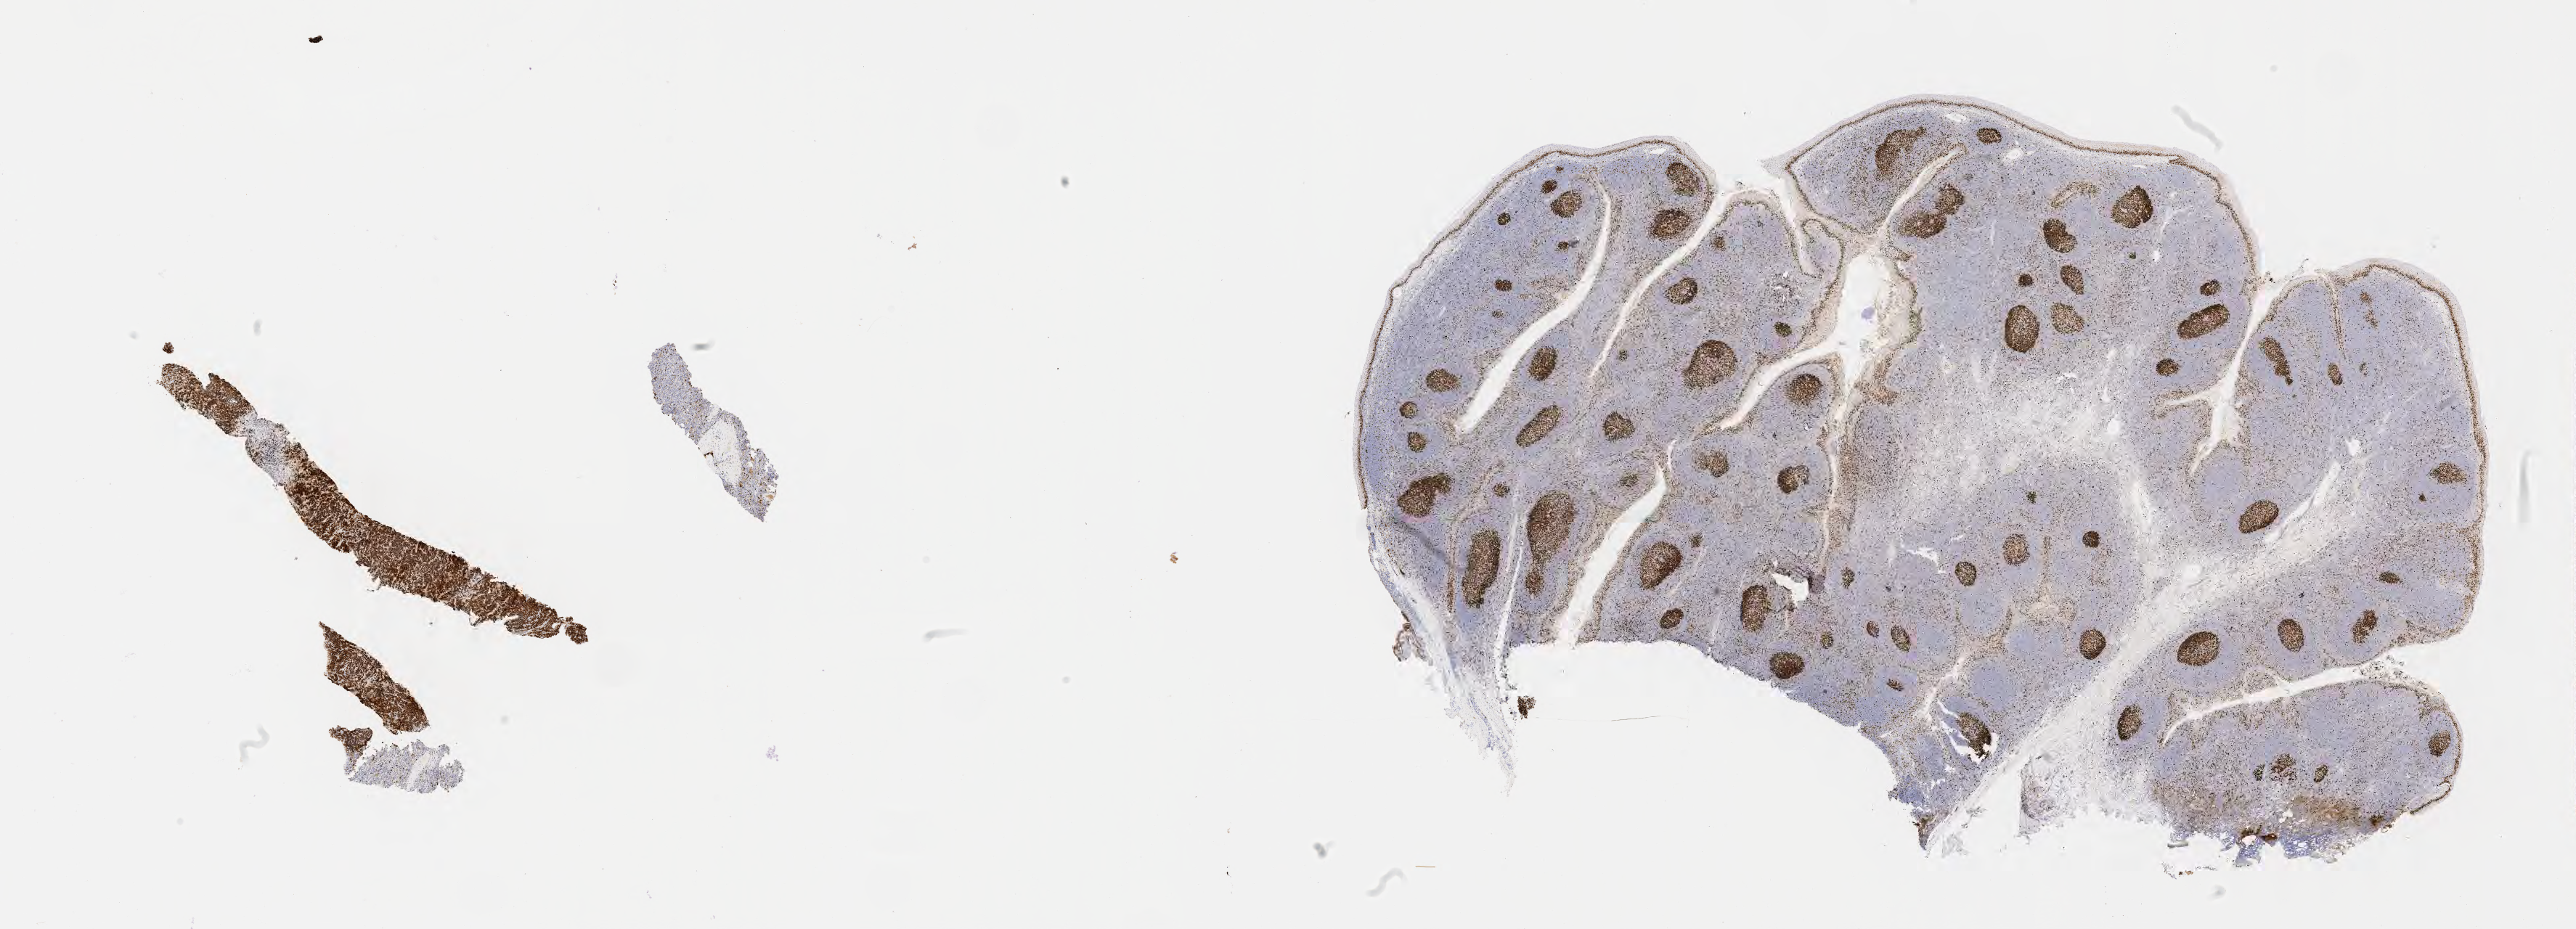
Immunohistochemistry (IHC) whole-slide image stained for Ki-67 — whole scanned area (about 28.7 x 10.3 mm) shown as a low-resolution overview, tumor tissue. Patient: male, 13 years old.
Diagnosis: Diffuse large B-cell lymphoma, NOS.